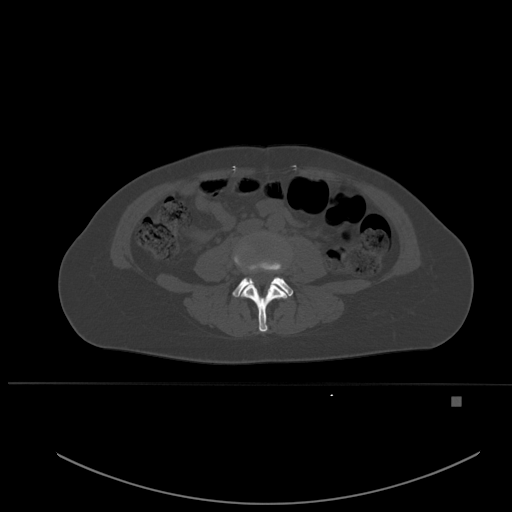
CT including the spine, one axial slice. Position 183 of 651 along the scan axis. Bone window (W 1800 / L 400 HU). 512 × 512 image matrix. Patient: female, 49 years. From the clinical record (not read from this slice): primary cancer: breast; vertebrae with lytic lesions (as recorded): L3, T12, L4.
Structures marked on this image (semi-automatically segmented with operator editing):
- L3 vertebra: bounding box [x1, y1, x2, y2] px = [234, 248, 288, 332]
- L4 vertebra: [233, 261, 293, 297]